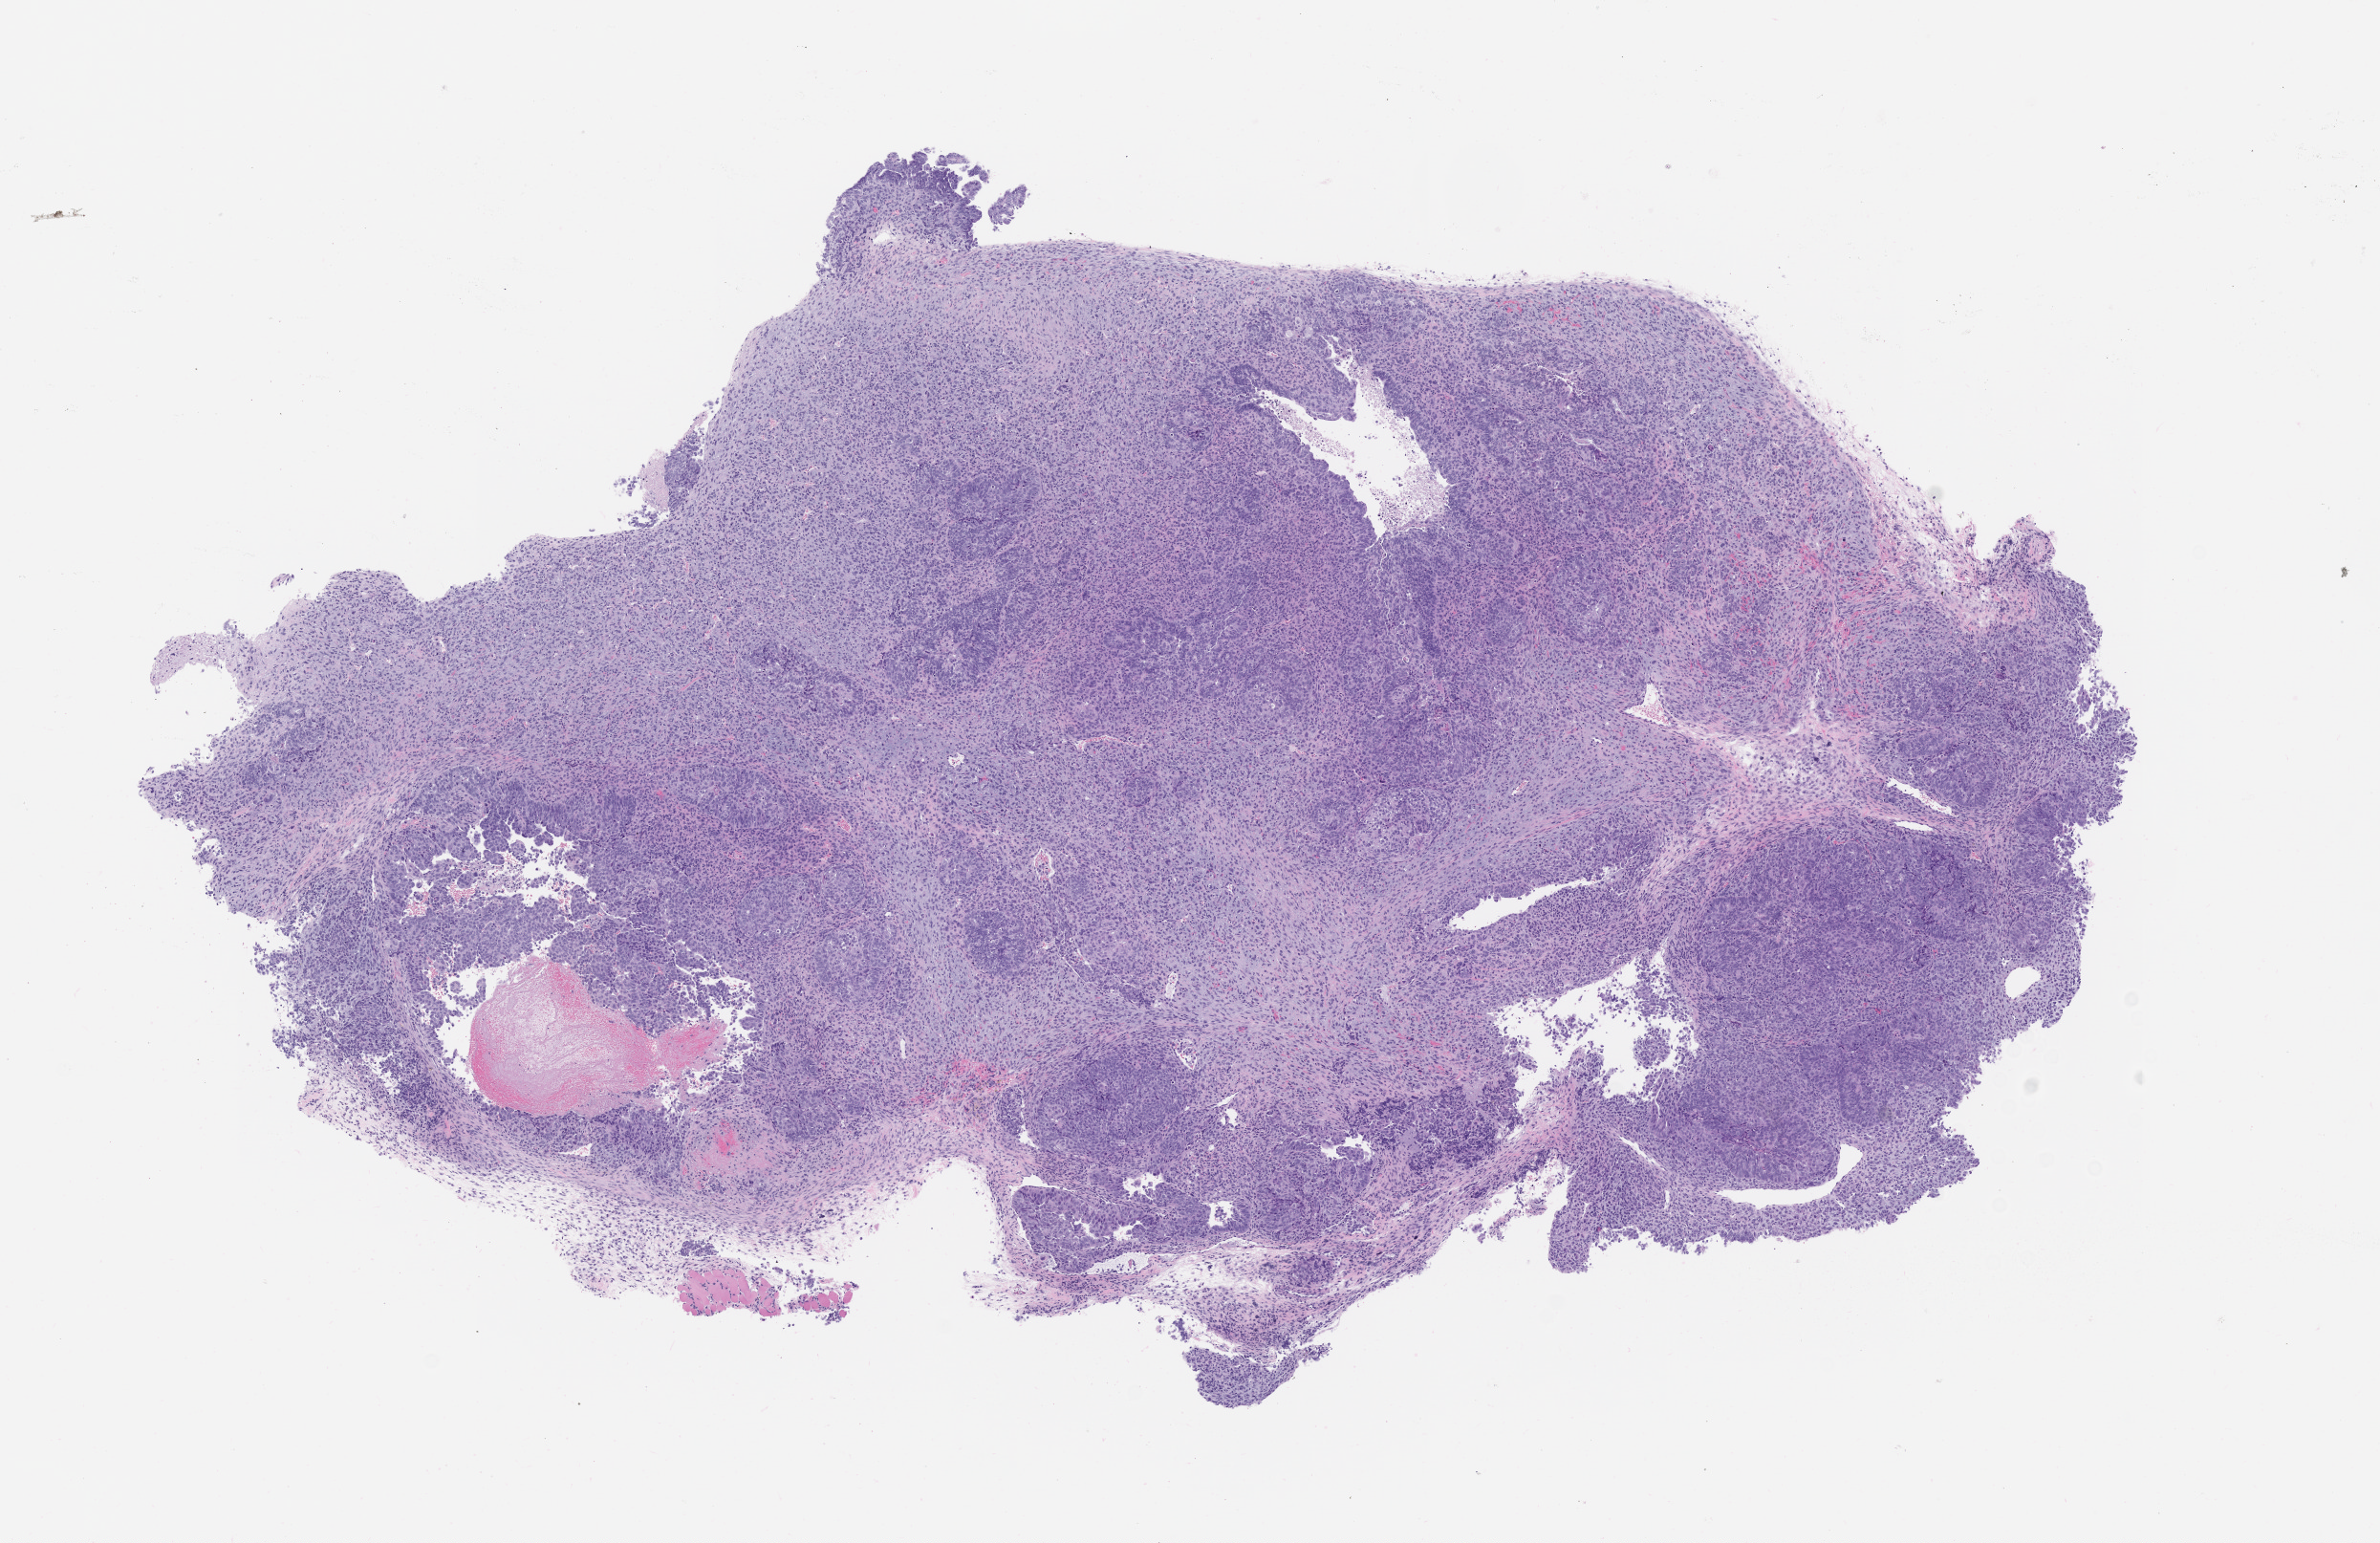
H&E whole-slide image of a patient-derived xenograft (PDX) tumor grown in a mouse, passage 1, whole scanned area (about 10.0 x 6.5 mm) shown as a low-resolution overview. Formalin-fixed paraffin-embedded section. Originating tumor site category: female genital tract.
* originating patient diagnosis: Carcinosarcoma